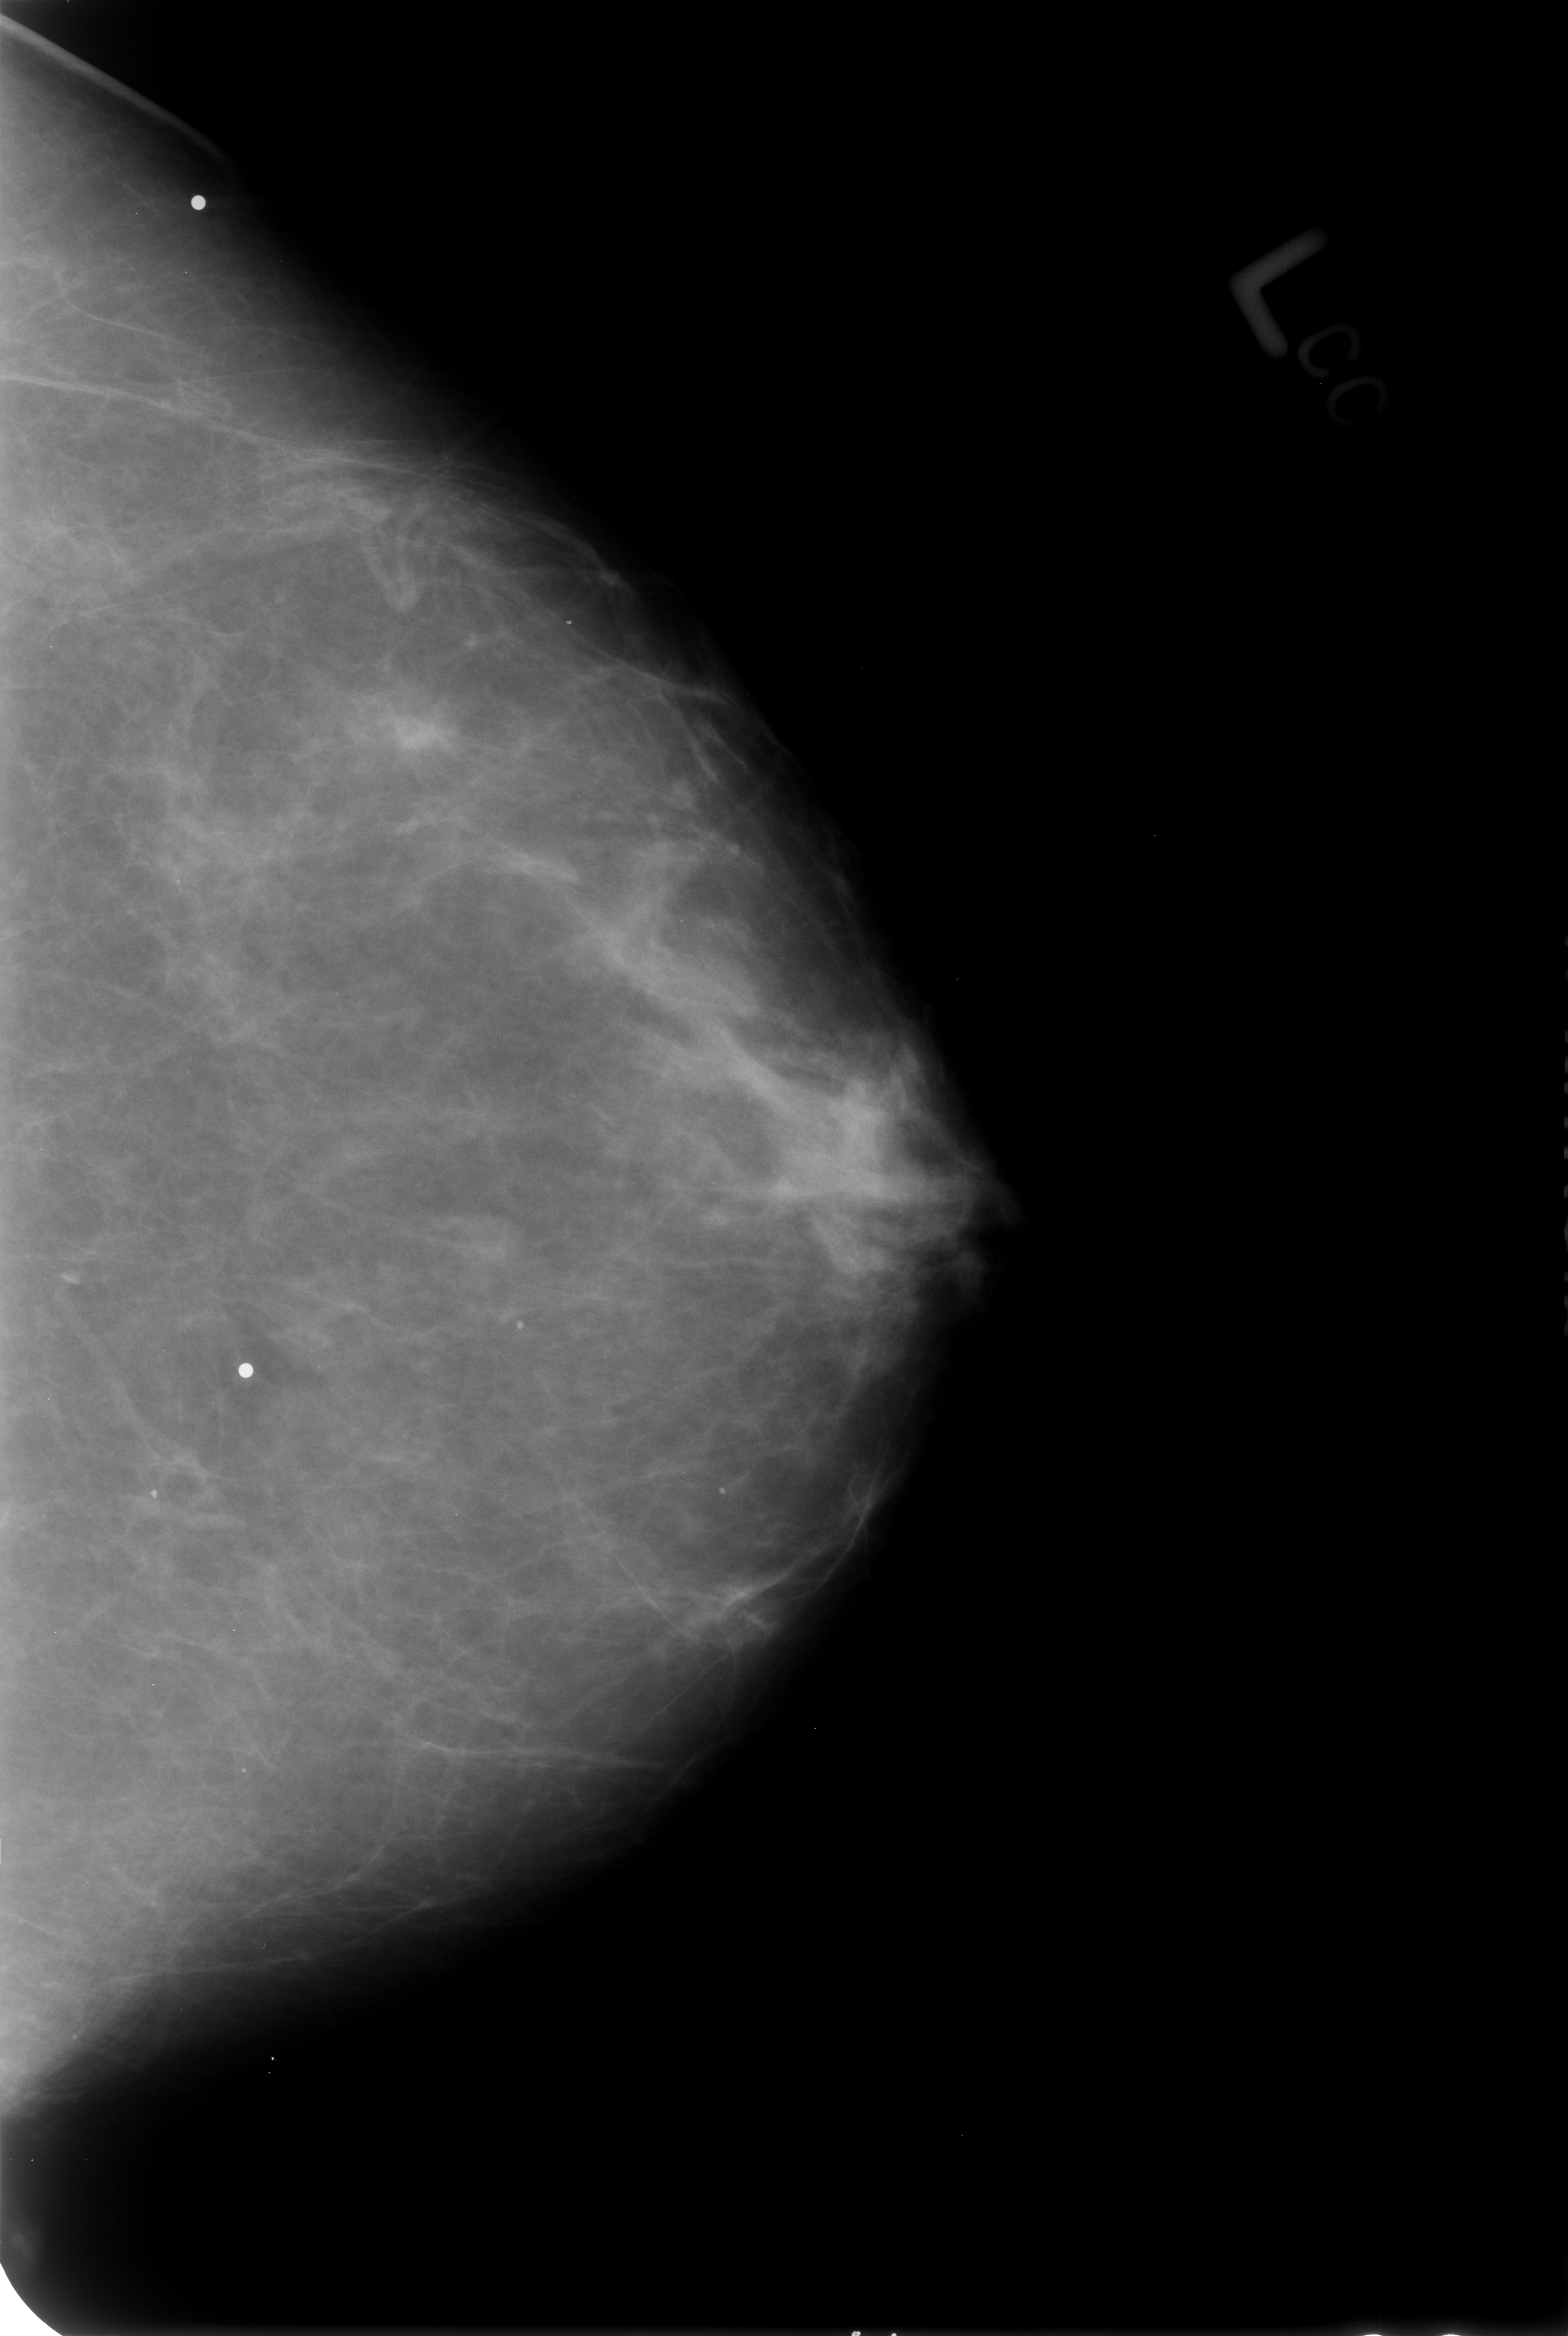
Mammogram (digitized film). Left breast. Craniocaudal (CC) view. BI-RADS breast density category 2 (scale 1–4). 1568 × 2336 image matrix.
Expert-marked regions of interest on this image (one box per marked abnormality):
- Finding 1 of 3: calcifications, morphology punctate; BI-RADS assessment category 2; benign; no additional work-up was recommended (outcome (as recorded, no biopsy): benign without callback): bounding box <211,1738,289,1817> (left, top, right, bottom; pixels)
- Finding 2 of 3: calcifications, morphology punctate; BI-RADS assessment category 2; outcome (as recorded, no biopsy): benign without callback (not worked up further): <471,1295,558,1374>
- Finding 3 of 3: calcifications, morphology punctate; BI-RADS assessment category 2; subtlety rating 3 on a 1 (subtle) to 5 (obvious) scale; benign; no additional work-up was recommended (outcome (as recorded, no biopsy): benign without callback): <686,1458,757,1533>